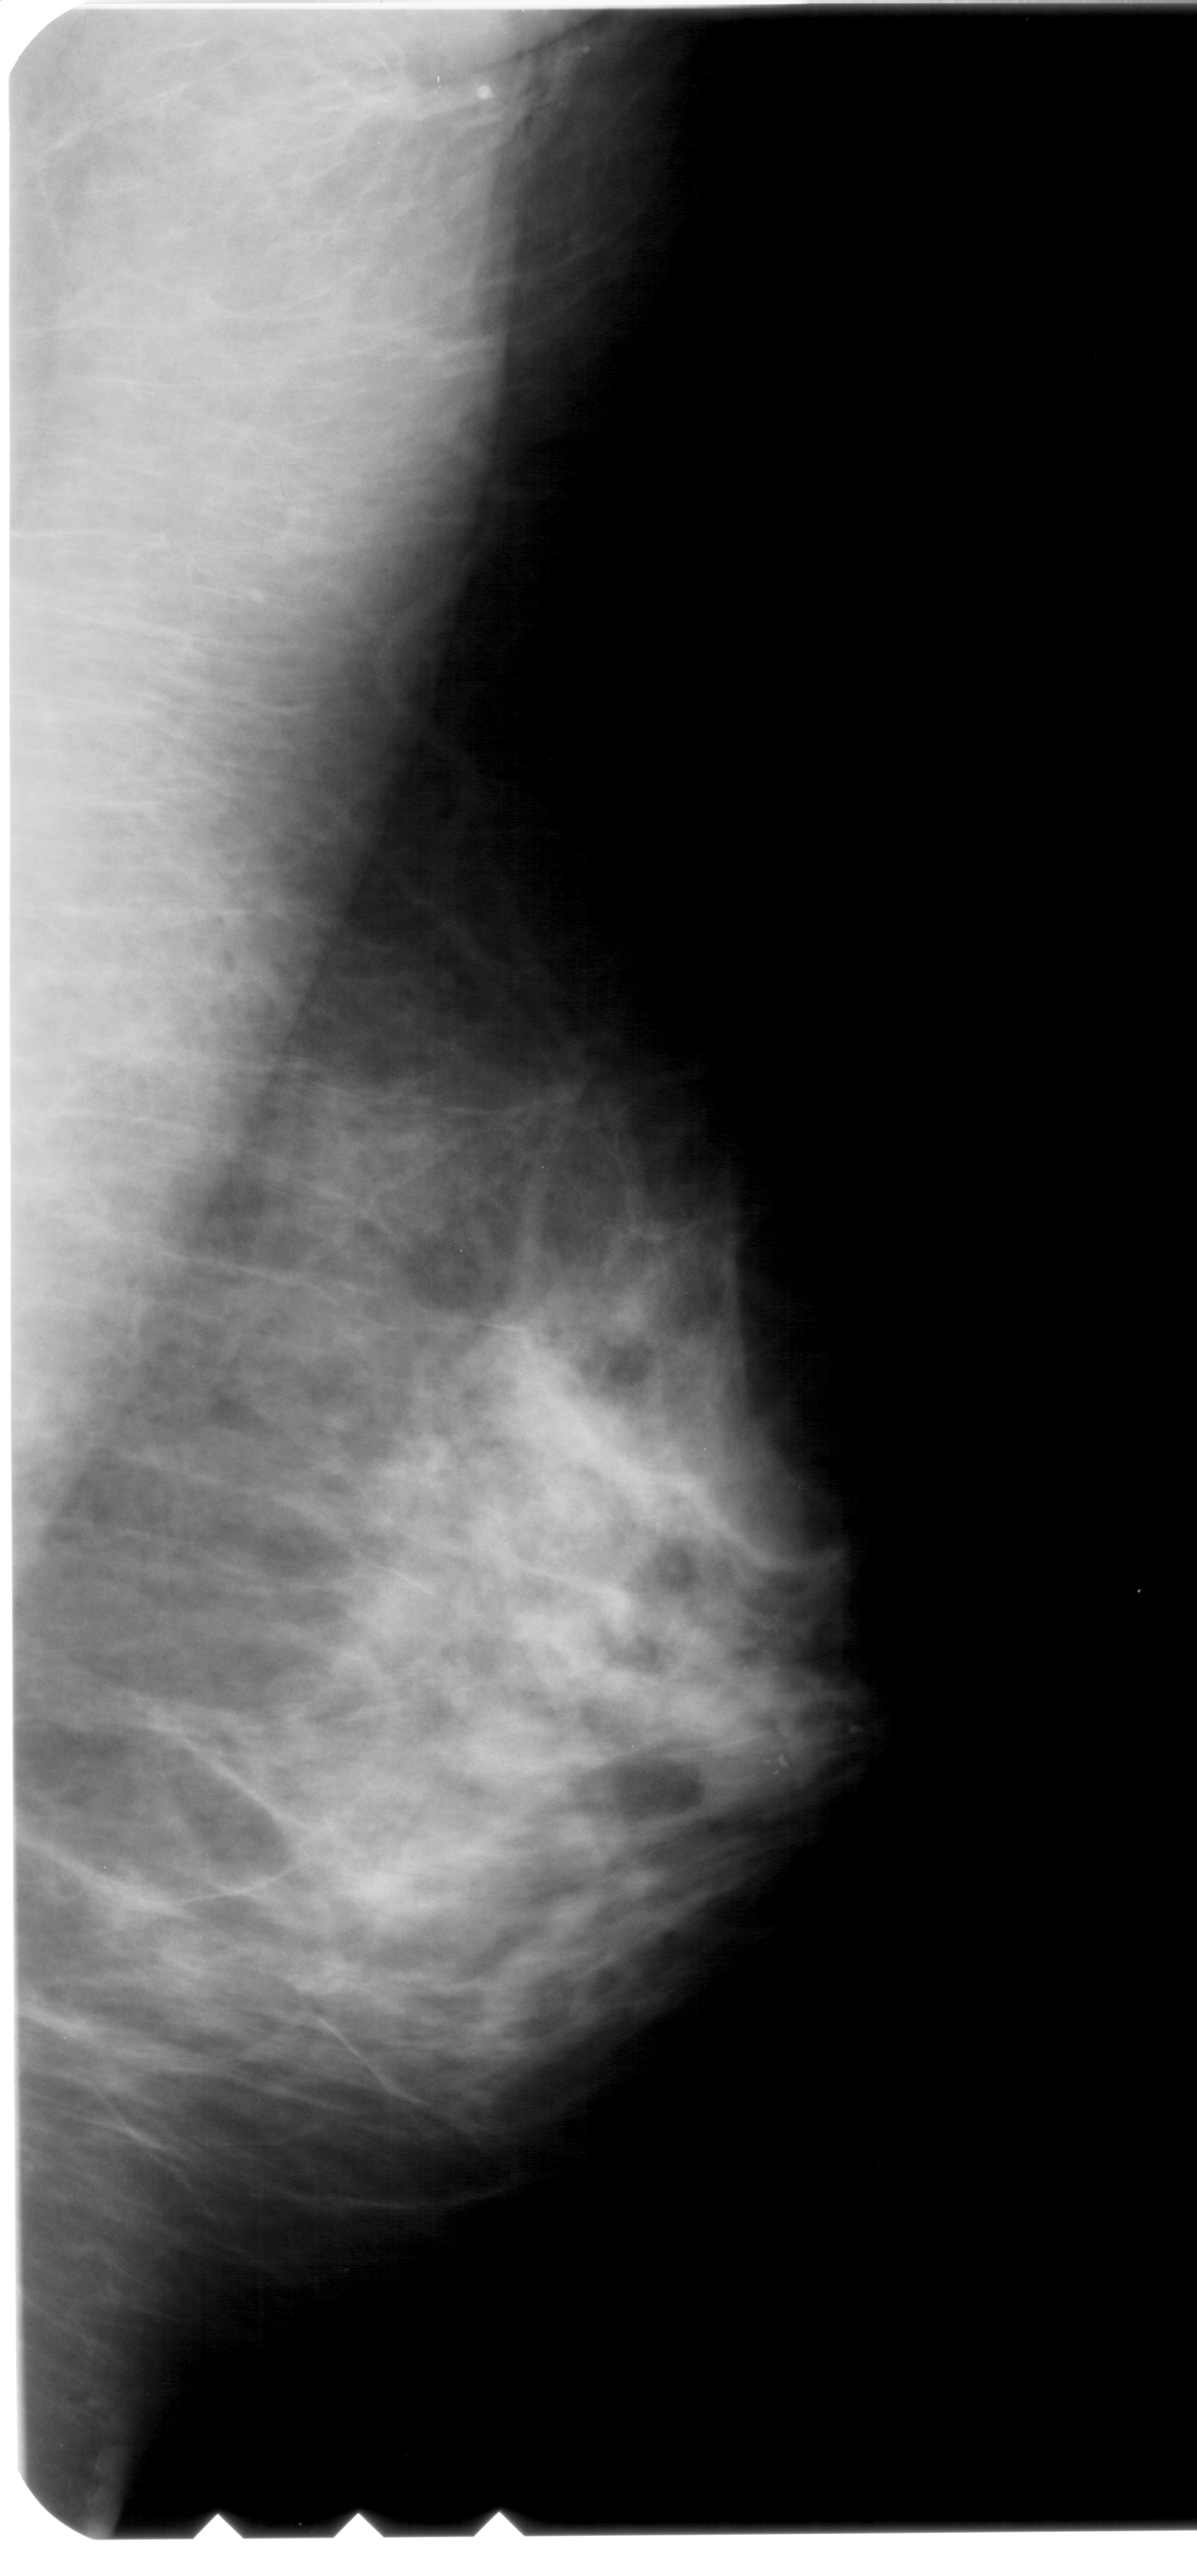
Scanned film-screen mammogram; right breast; mediolateral oblique (MLO) view; breast composition: extremely dense (BI-RADS density category 4 of 4).
Radiologist-marked abnormalities on this image: calcifications, morphology amorphous, distribution clustered; BI-RADS assessment category 4; pathology result (as recorded, not read from the image): benign.